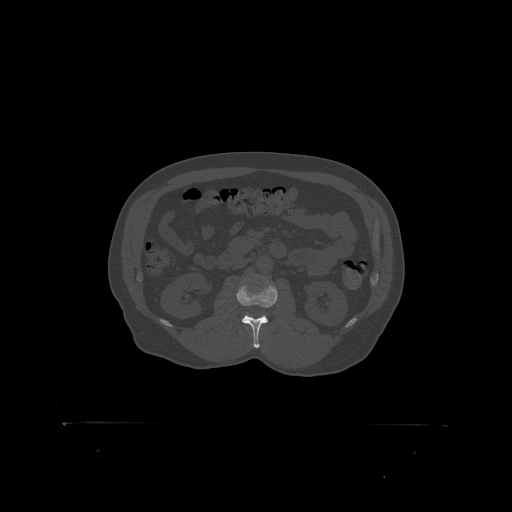
CT including the spine, one axial slice. Slice 288 of 399 in the series (ordered by position). Bone window (W 1800 / L 400 HU). 1.25 mm slice thickness. 512 × 512 image matrix, field of view 650 × 650 mm. Male patient, age 46 years. From the clinical record (not read from this slice): primary cancer: skin.
Annotated regions visible in this slice (semi-automatic segmentation, software-assisted and operator-edited):
- L2 vertebra: bounding box <237,284,278,319> (left, top, right, bottom; pixels)